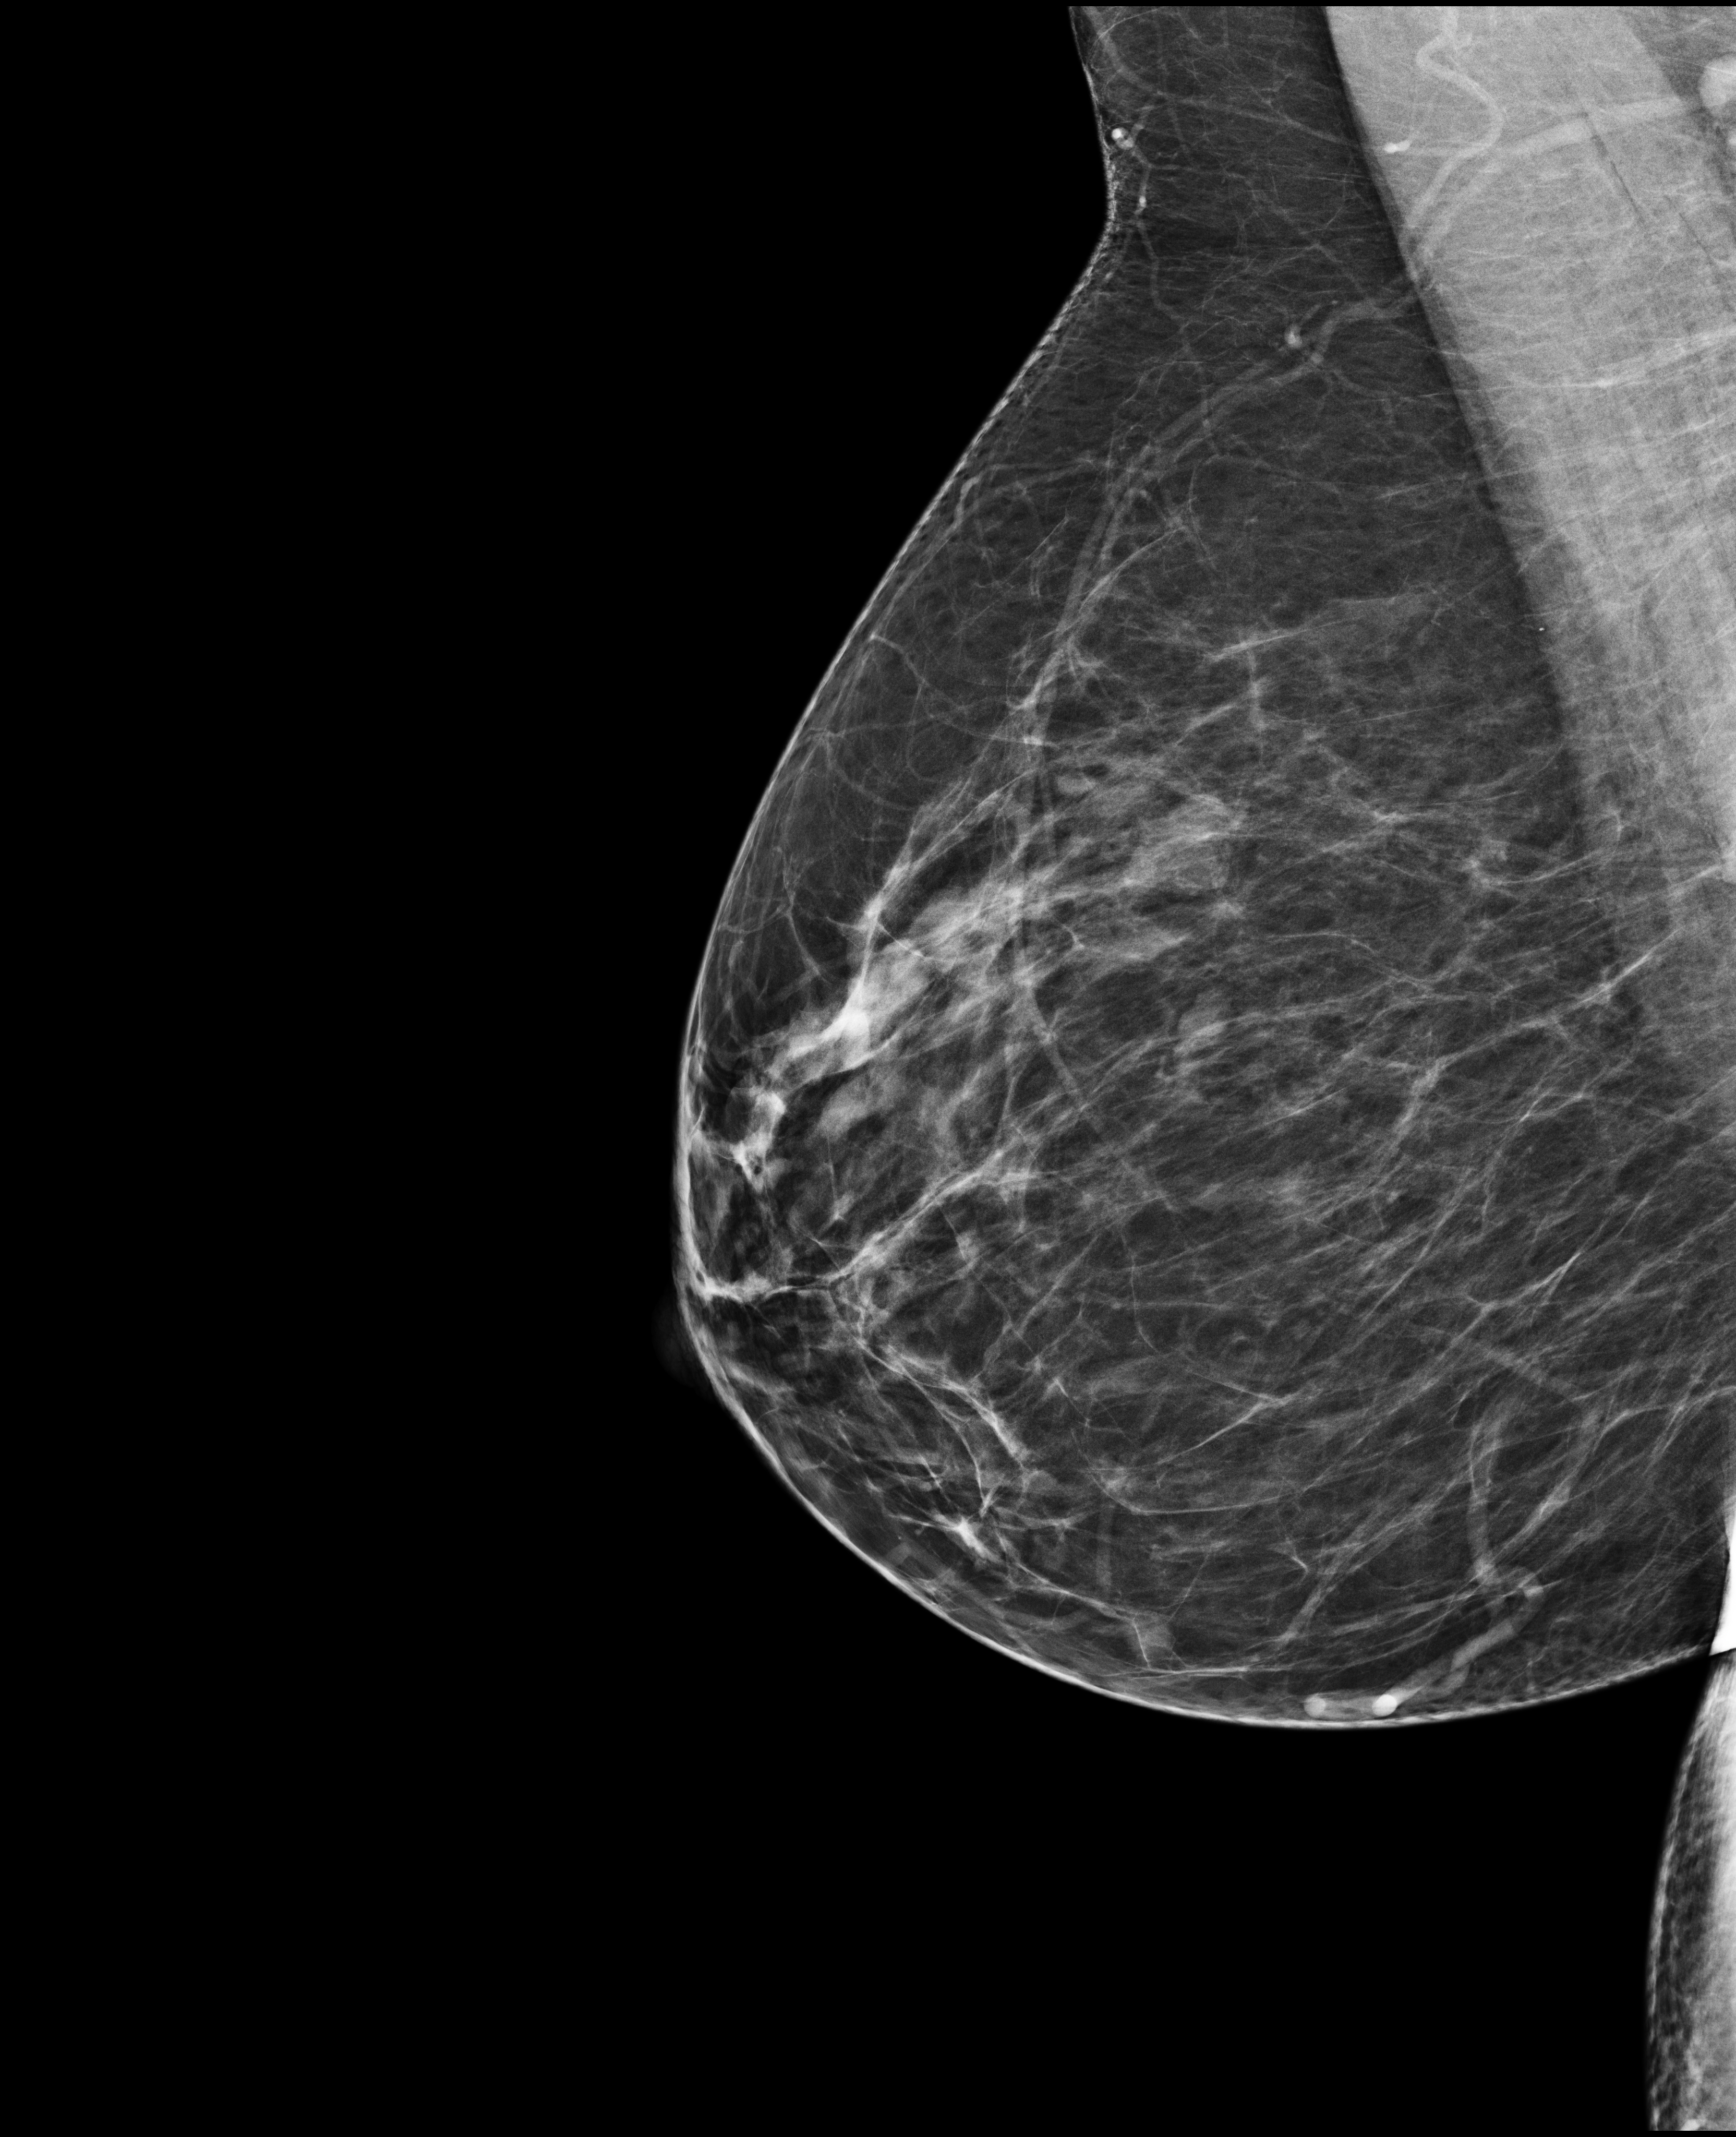
Screening examination. Patient: female, 65 years.
Image type: full-field digital mammogram. Breast: right. Projection: mediolateral oblique (MLO) view.